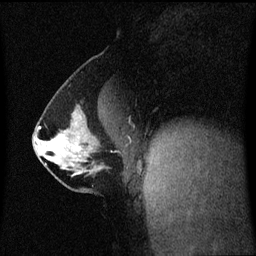
Breast MRI (dynamic contrast-enhanced), one sagittal slice. Position 30 of 60 along the scan axis. Dynamic contrast-enhanced series, image 2 of 3 at this slice position (ordered by acquisition). 1.5 T. TE 4.2 ms, TR 8.4 ms. 2 mm slice thickness. 256 × 256 image matrix. Female patient, age 40 years. From the clinical record (not read from this slice): setting: breast cancer imaged before/during neoadjuvant chemotherapy; receptor status: triple-negative.
Annotated regions visible in this slice (semi-automatically segmented with operator editing):
- analysis volume of interest (the breast-tissue region the enhancement analysis was run in; not a lesion): bounding box (x1, y1, x2, y2) in pixels: (33, 112, 109, 188)
- tumour enhancement mask (voxels above the 70 % enhancement threshold inside the analysis volume of interest): (39, 127, 80, 151)